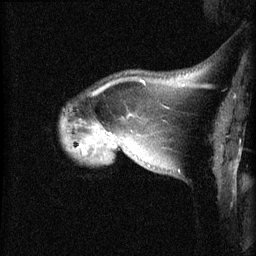
Breast MRI (dynamic contrast-enhanced), one sagittal slice; position 9 of 60 along the scan axis; dynamic contrast-enhanced series, image 2 of 3 at this slice position (ordered by acquisition); 1.5 T; TE 4.2 ms, TR 8.2 ms; 2.1 mm slice thickness; 256 × 256 image matrix, field of view 180 × 180 mm. Female patient, age 50 years.
Annotated regions visible in this slice (semi-automatically segmented with operator editing):
- analysis volume of interest (the breast-tissue region the enhancement analysis was run in; not a lesion): box from (x=61, y=113) to (x=169, y=173) px
- tumour enhancement mask (voxels above the 70 % enhancement threshold inside the analysis volume of interest): (x=80, y=133)–(x=111, y=153)